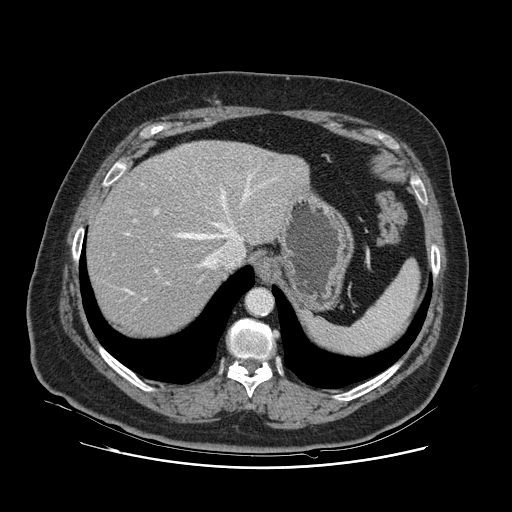
Contrast-enhanced abdominal CT, one axial slice; position 96 of 132 along the scan axis; 120 kVp; intravenous contrast given; soft-tissue window (W 400 / L 40 HU); 512 × 512 image matrix, field of view 391 × 391 mm. Female patient, age 73 years. From the clinical record (not read from this slice): diagnosis: colorectal cancer liver metastases, imaged before liver resection; multiple liver metastases: no; largest metastasis: 7 cm.
Structures marked on this image (expert manual segmentation):
- hepatic veins: bounding box [x1, y1, x2, y2] px = [113, 174, 275, 301]
- liver: [88, 142, 306, 335]
- planned liver remnant (the part of the liver to remain after resection): [88, 161, 226, 337]
- portal vein (with intrahepatic branches): [154, 208, 159, 273]